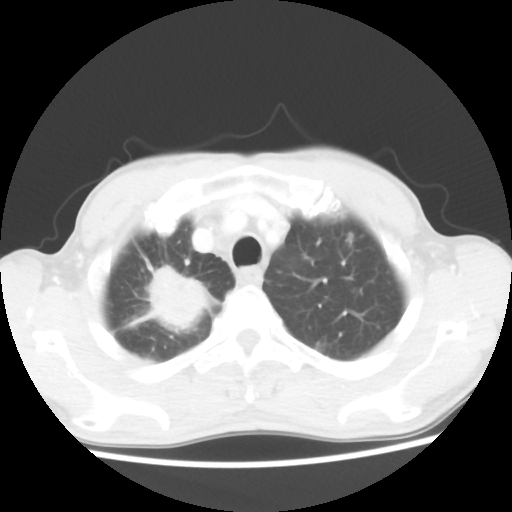
Chest CT, one axial slice. Slice 44 of 52 in the series (ordered by position). Reconstruction kernel STANDARD. Lung window (W 1500 / L -600 HU). 512 × 512 image matrix. Male patient, age 66 years. From the clinical record (not read from this slice): clinical TNM (as recorded): T2 N0 M1a.
Structures marked on this image (rectangle marked by the reading radiologist):
- lung tumour (recorded histology: adenocarcinoma): bounding box <138,260,219,340> (left, top, right, bottom; pixels)